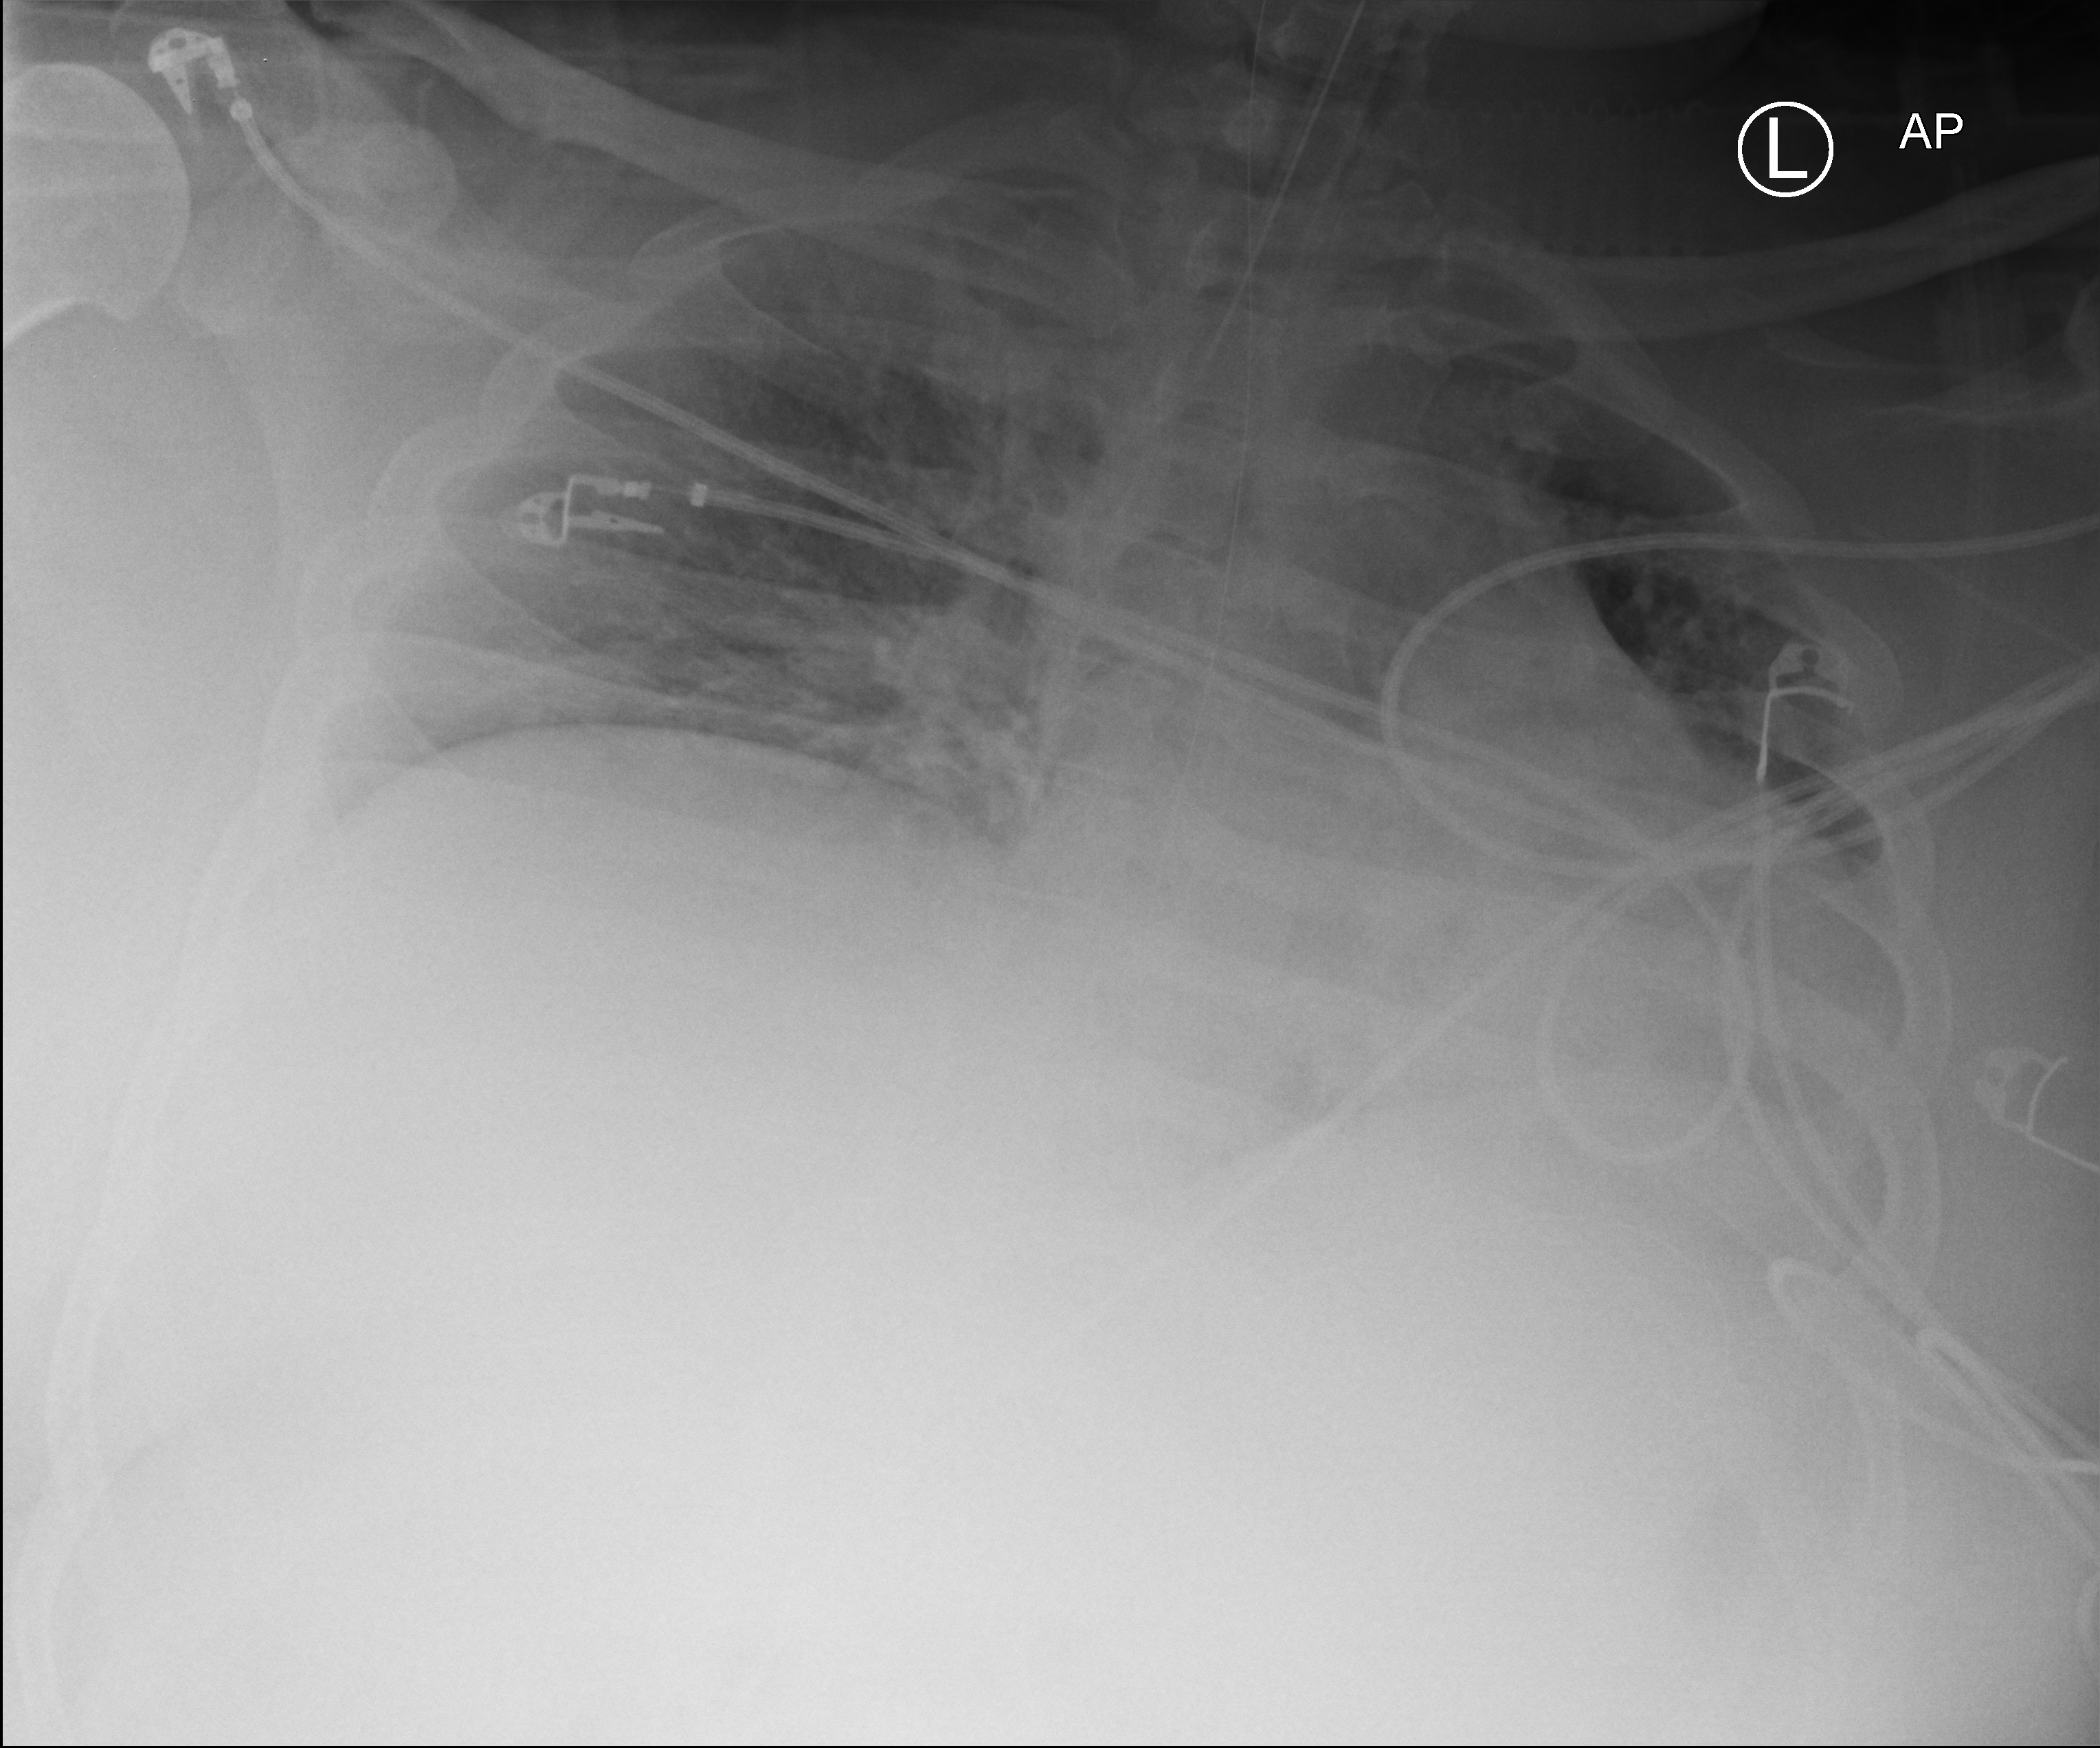
Chest X-ray (portable), anteroposterior (AP) projection. Male patient hospitalised with COVID-19, age 18–59 years.
From the hospital-stay record, not from the radiograph (when in the stay this image was taken is not recorded): admitted to intensive care during this hospital stay: yes; mechanically ventilated during this hospital stay: yes.